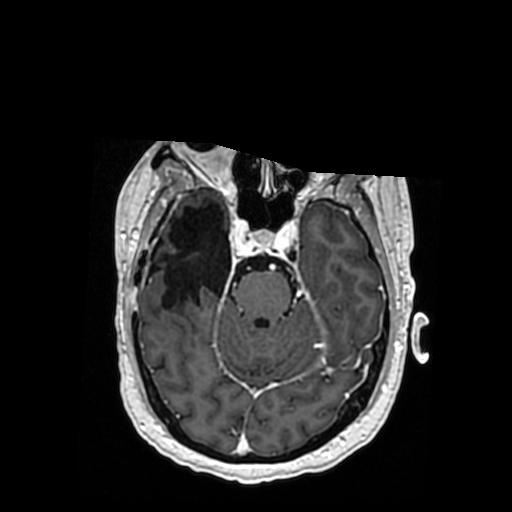
Brain MRI from a brain-tumour surgery series, one axial slice; position 233 of 364 along the scan axis; T1-weighted post-contrast; 0.5 mm slice thickness; 512 × 512 image matrix, field of view 260 × 260 mm. From the clinical record (not read from this slice): histopathology: Oligodendroglioma; WHO grade: 3; IDH mutation: yes; tumour location: Right Posterior Temporal Inferior Parietal.
Annotated regions visible in this slice (manually delineated by an expert):
- previous resection cavity: box from (x=161, y=205) to (x=231, y=307) px